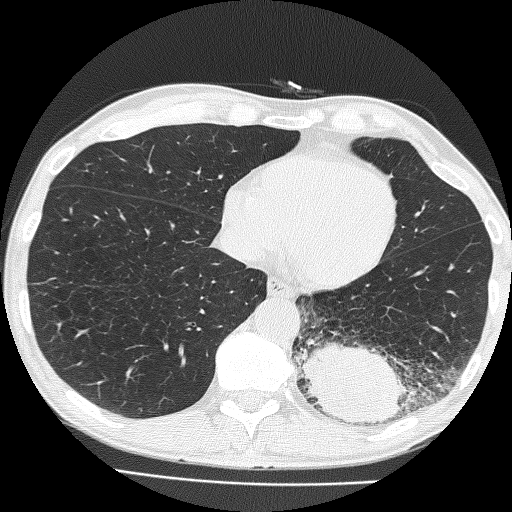
Chest CT (low-dose screening protocol), one axial image. Baseline screening round. Lung window (W 1500 / L -600 HU). 512 × 512 image matrix. Male, age 58 years at enrolment.
Expert reader's lesion annotation, bounding box <291,296,429,435> (left, top, right, bottom; pixels). The screening reader recorded 2 non-calcified nodules or masses ≥4 mm on this exam (left lower lobe, left upper lobe); which of them this box marks is not recorded. Official screen result: positive, change unspecified: nodule(s) >= 4 mm or enlarging nodule(s), mass(es), or other non-specific abnormalities suspicious for lung cancer. Lung cancer was diagnosed 39 days after this screen: non-small cell carcinoma, left lower lobe, poorly differentiated (G3), stage IV (AJCC 6th edition), 74 mm at pathology.